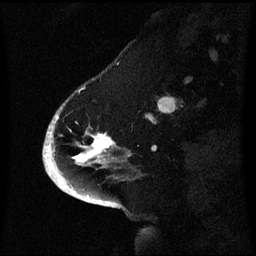
Breast MRI (dynamic contrast-enhanced), one sagittal slice; position 18 of 60 along the scan axis; dynamic contrast-enhanced series, image 2 of 3 at this slice position (ordered by acquisition); 1.5 T; TE 4.2 ms, TR 8.4 ms; 2.1 mm slice thickness; 256 × 256 image matrix. Female patient, age 53 years. From the clinical record (not read from this slice): setting: breast cancer imaged before/during neoadjuvant chemotherapy; receptor status: HR-positive, HER2-negative.
Outlined on this slice (semi-automatically segmented with operator editing):
- analysis volume of interest (the breast-tissue region the enhancement analysis was run in; not a lesion): bounding box [x1, y1, x2, y2] px = [52, 104, 124, 171]
- tumour enhancement mask (voxels above the 70 % enhancement threshold inside the analysis volume of interest): [52, 116, 116, 169]